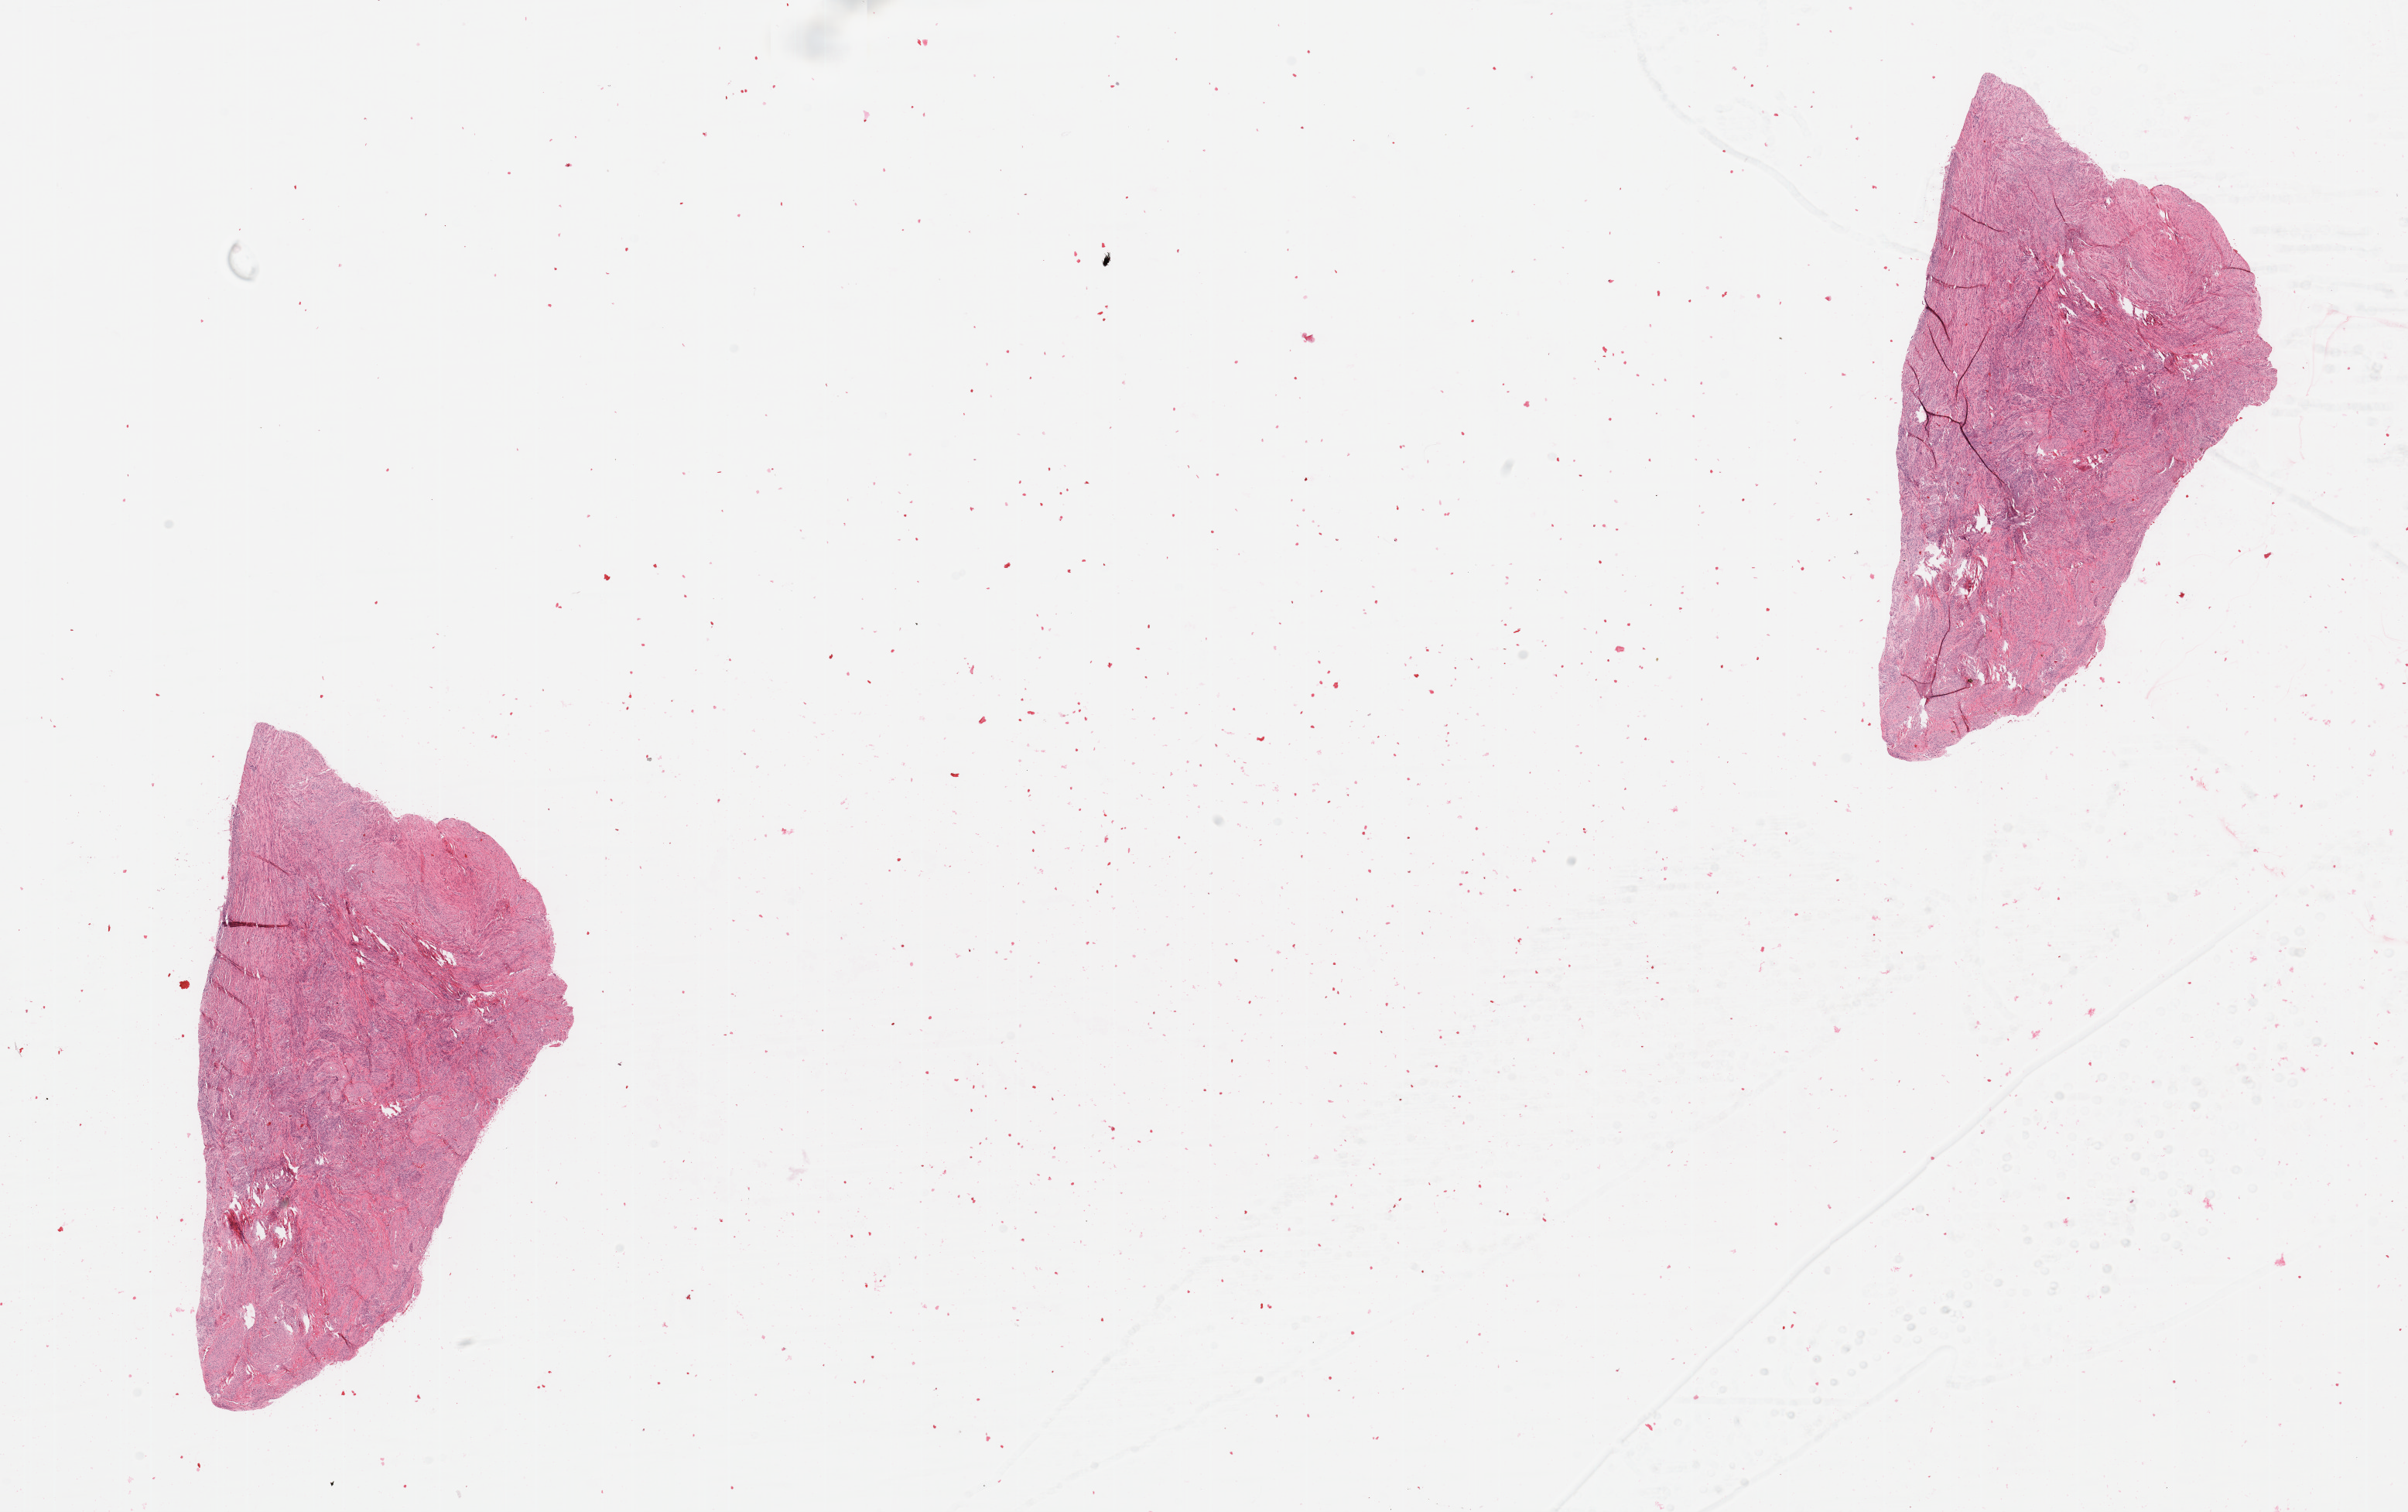
Whole-slide histology image, Hematoxylin and eosin (H&E) stained, whole scanned area (about 24.6 x 15.5 mm, slide scanned at 20x) shown as a low-resolution overview, uterus, normal (non-tumour) tissue. 74-year-old female patient.
This section: normal (non-tumour) tissue from the same patient. Patient diagnosis: Endometrioid adenocarcinoma, NOS.